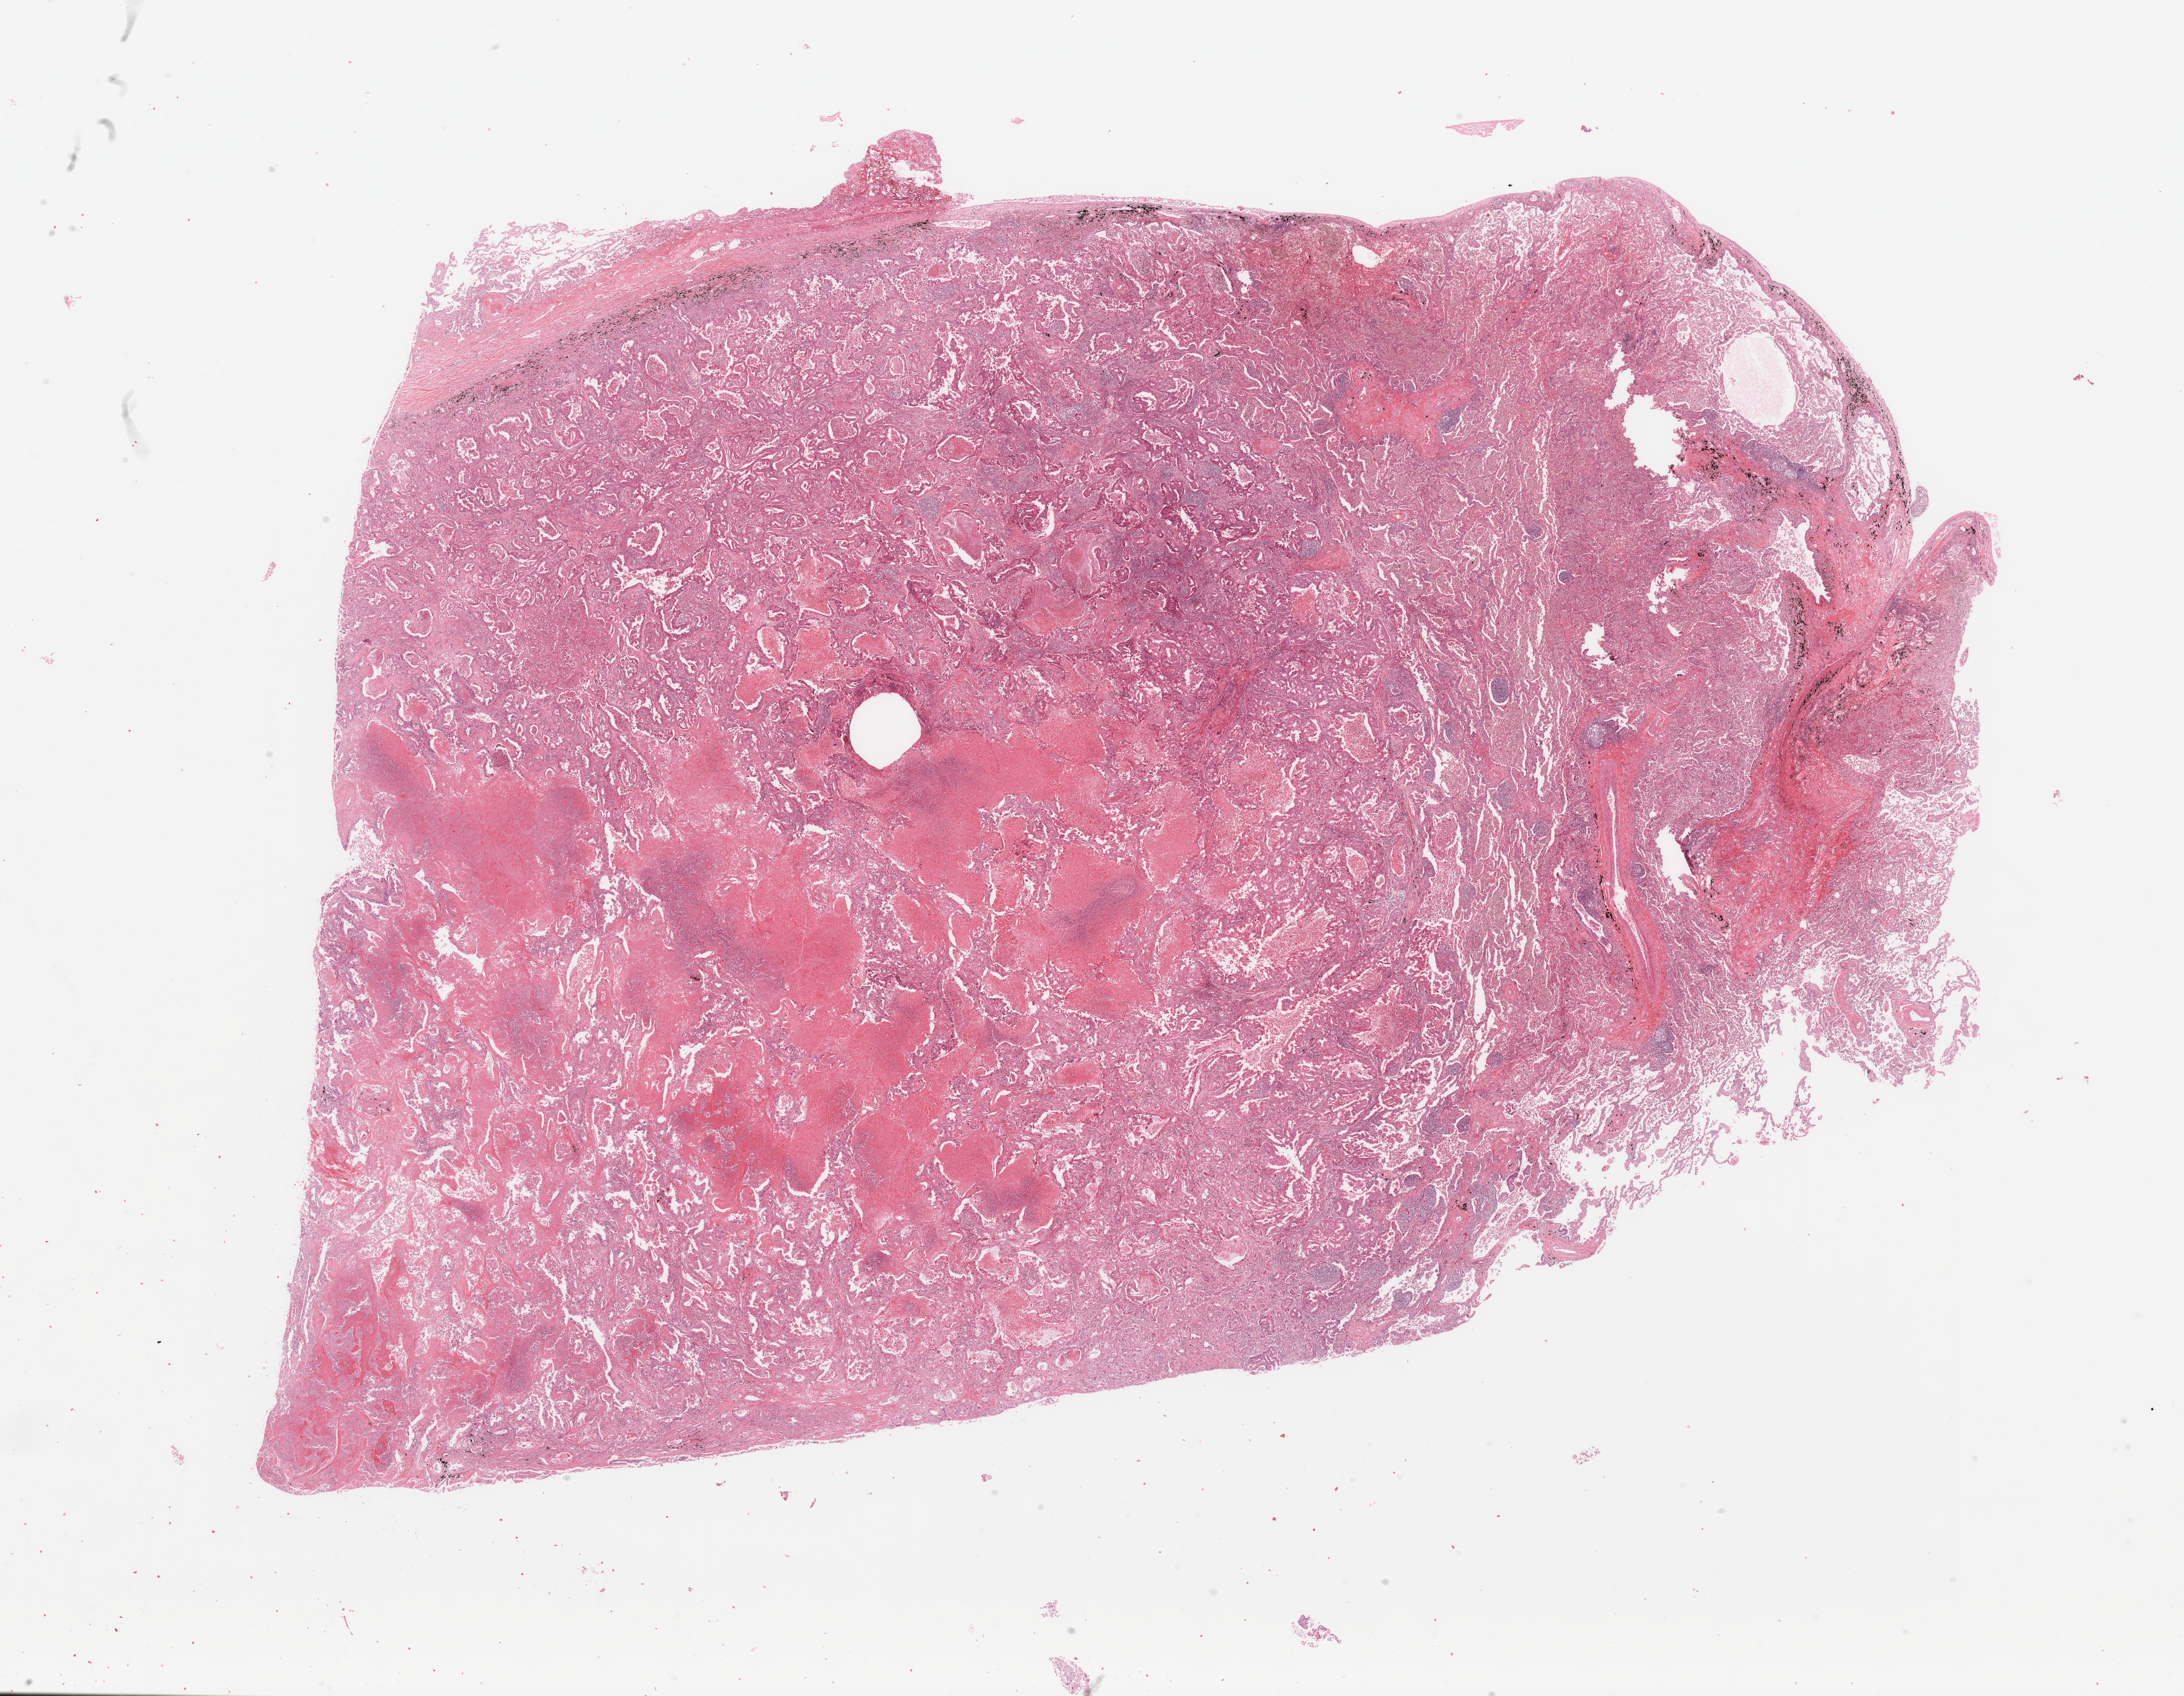
Hematoxylin and eosin (H&E) stained whole-slide image, shown as a low-resolution overview of the whole scanned area (about 28.5 x 22.2 mm); tumour tissue sample, lung. Patient: male, age 64 years. Histologic grade: G2 (moderately differentiated).
Histologic diagnosis: Adenocarcinoma, NOS. AJCC pathologic stage: IIB.